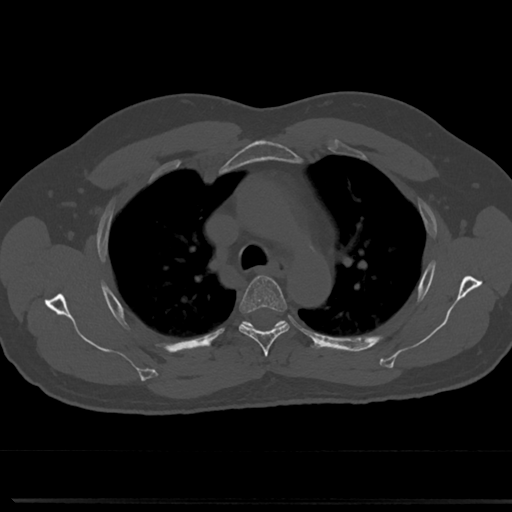
CT including the spine, one axial slice. Position 536 of 817 along the scan axis. Reconstruction kernel Br40s/3. Bone window (W 1800 / L 400 HU). 0.5 mm slice thickness. 512 × 512 image matrix. Male patient, age 61 years. Case-level facts recorded for this patient, not image findings: primary cancer: prostate.
Annotated regions visible in this slice (semi-automatically segmented with operator editing):
- T4 vertebra: bounding box <237,275,290,354> (left, top, right, bottom; pixels)
- T5 vertebra: <246,322,283,326>